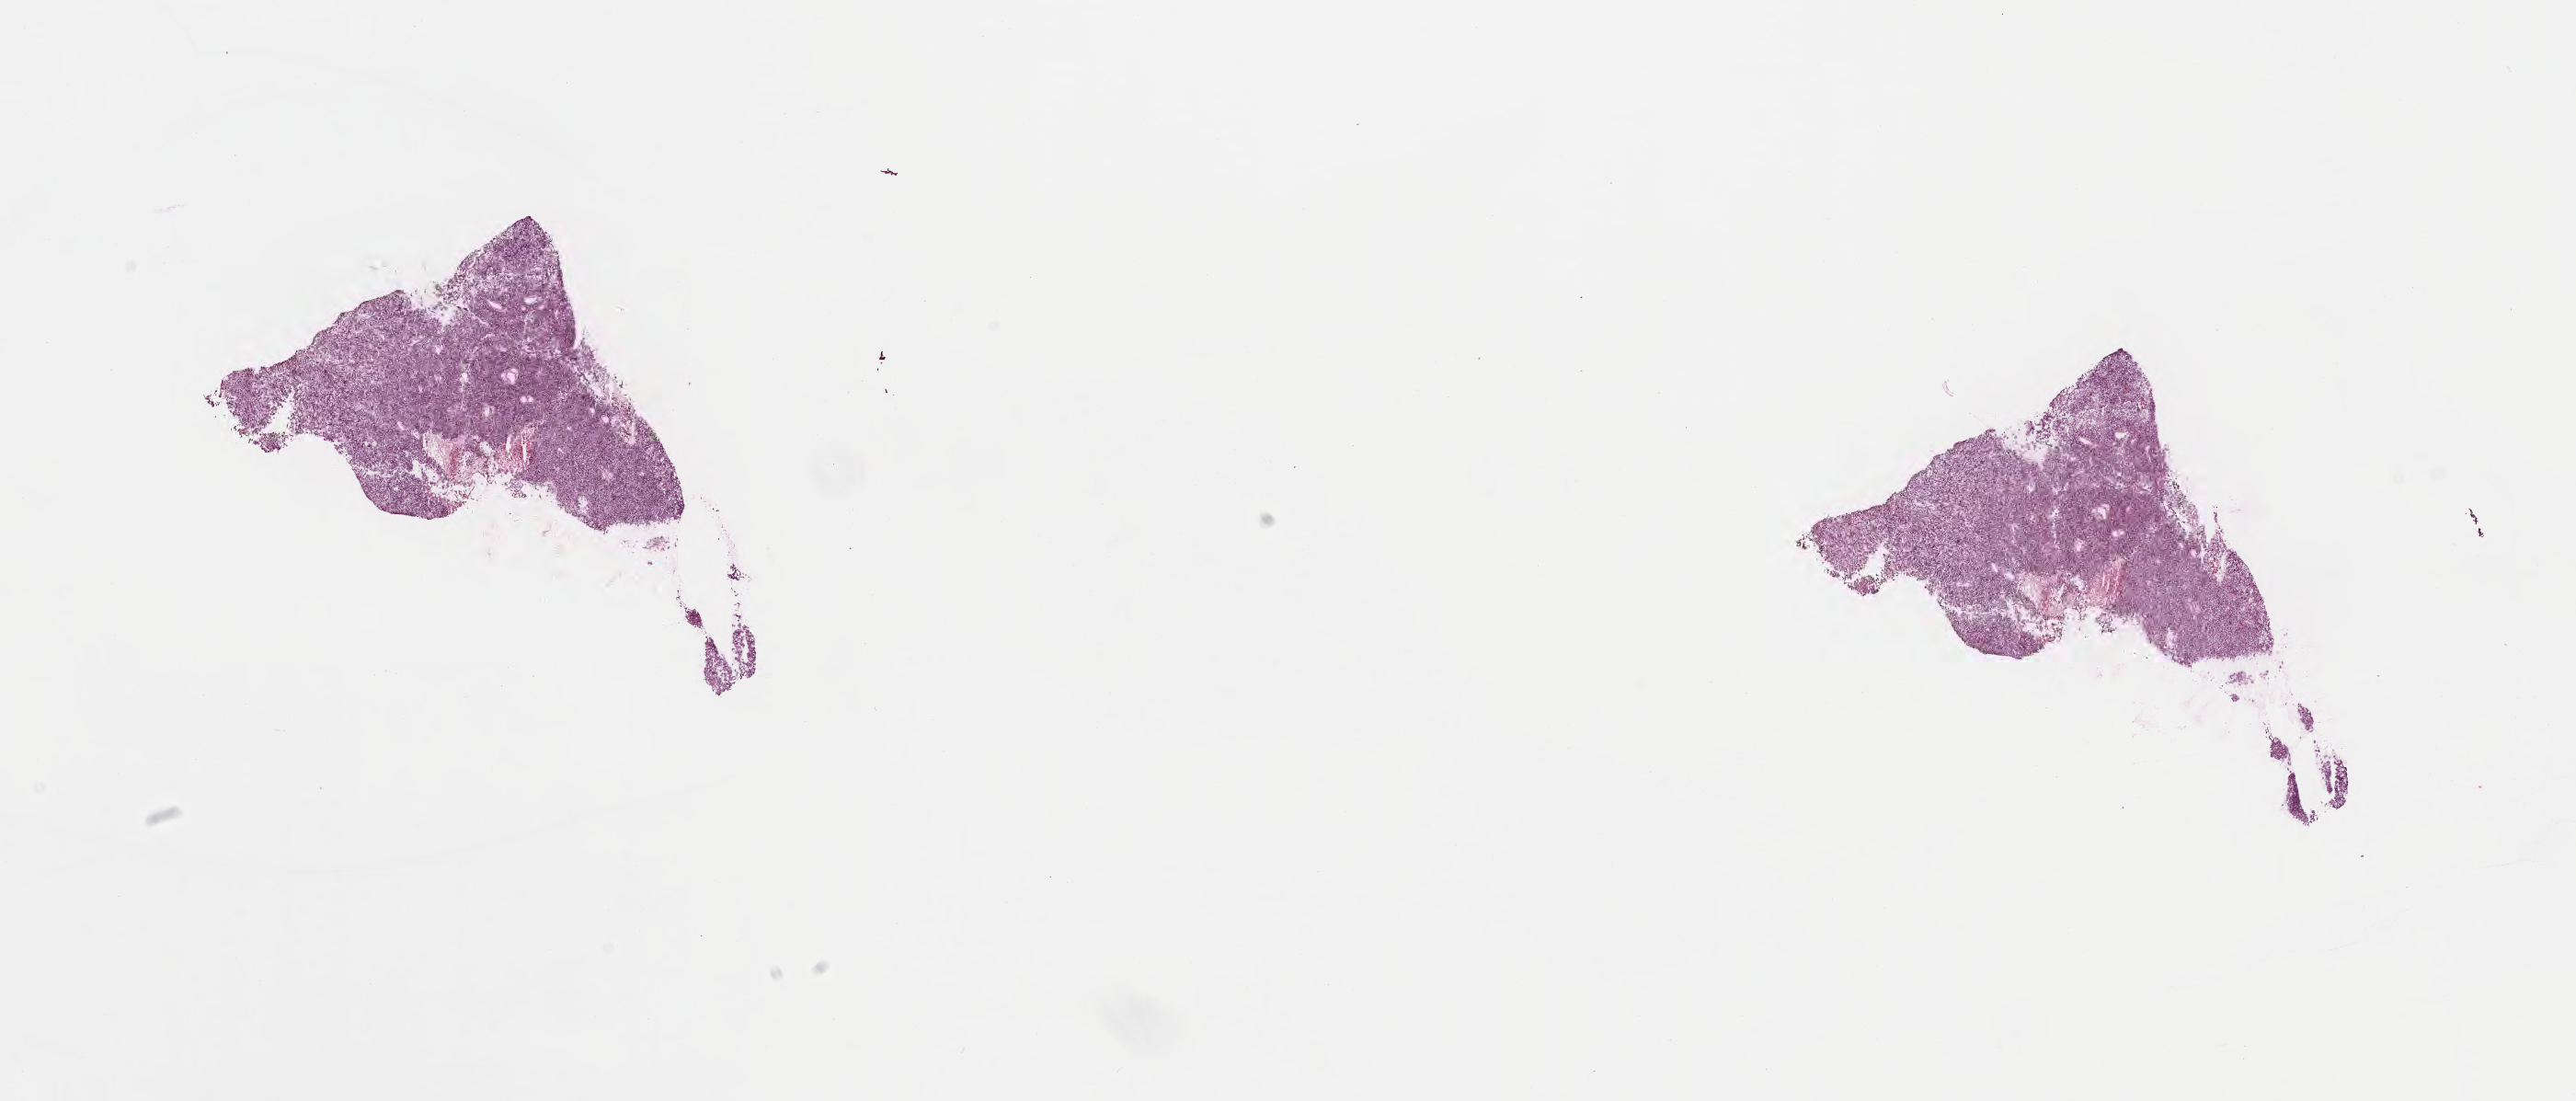
Whole-slide image, H&E stain — shown as a low-resolution overview of the whole scanned area (about 22.7 x 9.7 mm); frozen section; specimen: metastatic tumor tissue, resected from lymph node. Female, age 53 years at initial diagnosis. Slide review estimates, as recorded: tumor cells 90%, tumor nuclei 90%, stromal cells 8%, necrosis 2%, normal cells 0%. Inflammatory infiltration, as recorded: lymphocyte infiltration 2%, monocyte infiltration 1%, neutrophil infiltration 2%.
- patient diagnosis (primary): Malignant melanoma, NOS
- section: bottom of the tissue portion